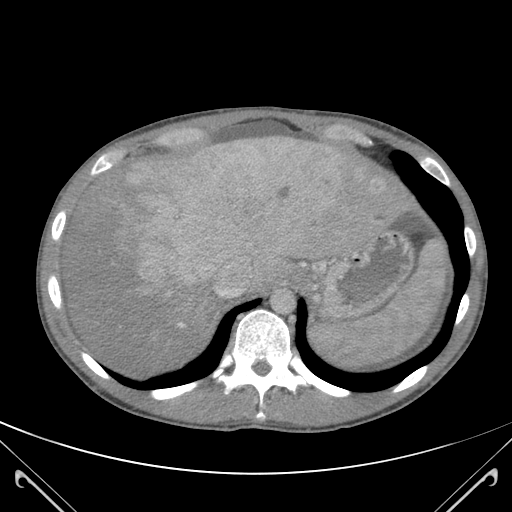
Contrast-enhanced abdominal CT (liver protocol), one axial slice. Position 96 of 118 along the scan axis. 120 kVp. Soft-tissue window (W 400 / L 40 HU). 512 × 512 image matrix. From the clinical record (not read from this slice): diagnosis: hepatocellular carcinoma (patient treated with transarterial chemoembolisation; whether this scan precedes or follows treatment is not stated here); TNM stage (as recorded): Stage-IIIB; Child-Pugh class: A; tumour nodularity: uninodular.
Structures marked on this image (semi-automatically segmented with operator editing):
- abdominal aorta: bounding box (x1, y1, x2, y2) in pixels: (273, 289, 295, 312)
- liver parenchyma outside the tumour (the mass and vessels are separate outlines, so this box may not span the whole liver): (65, 138, 393, 370)
- mass: (99, 138, 359, 296)
- liver vessels: (178, 146, 375, 327)